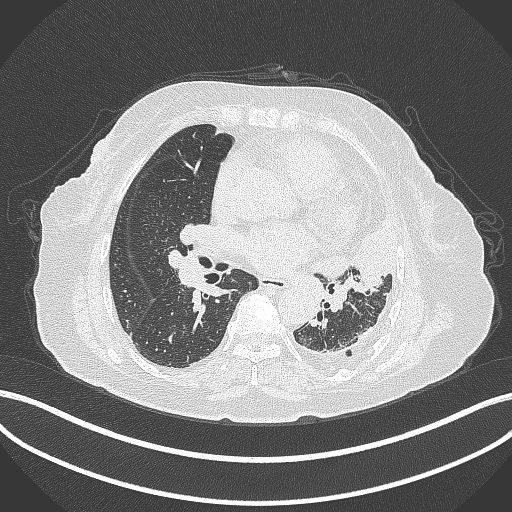
Chest CT, one axial slice. Slice 183 of 399 in the series (ordered by position). Reconstruction kernel B70f. 120 kVp. Lung window (W 1500 / L -600 HU). 1 mm slice thickness. 512 × 512 image matrix. Patient: female, 75 years. From the clinical record (not read from this slice): clinical TNM (as recorded): T3 N3 M1.
Structures marked on this image (bounding box drawn by a radiologist):
- lung tumour (recorded histology: adenocarcinoma): bounding box (x1, y1, x2, y2) in pixels: (309, 213, 399, 288)